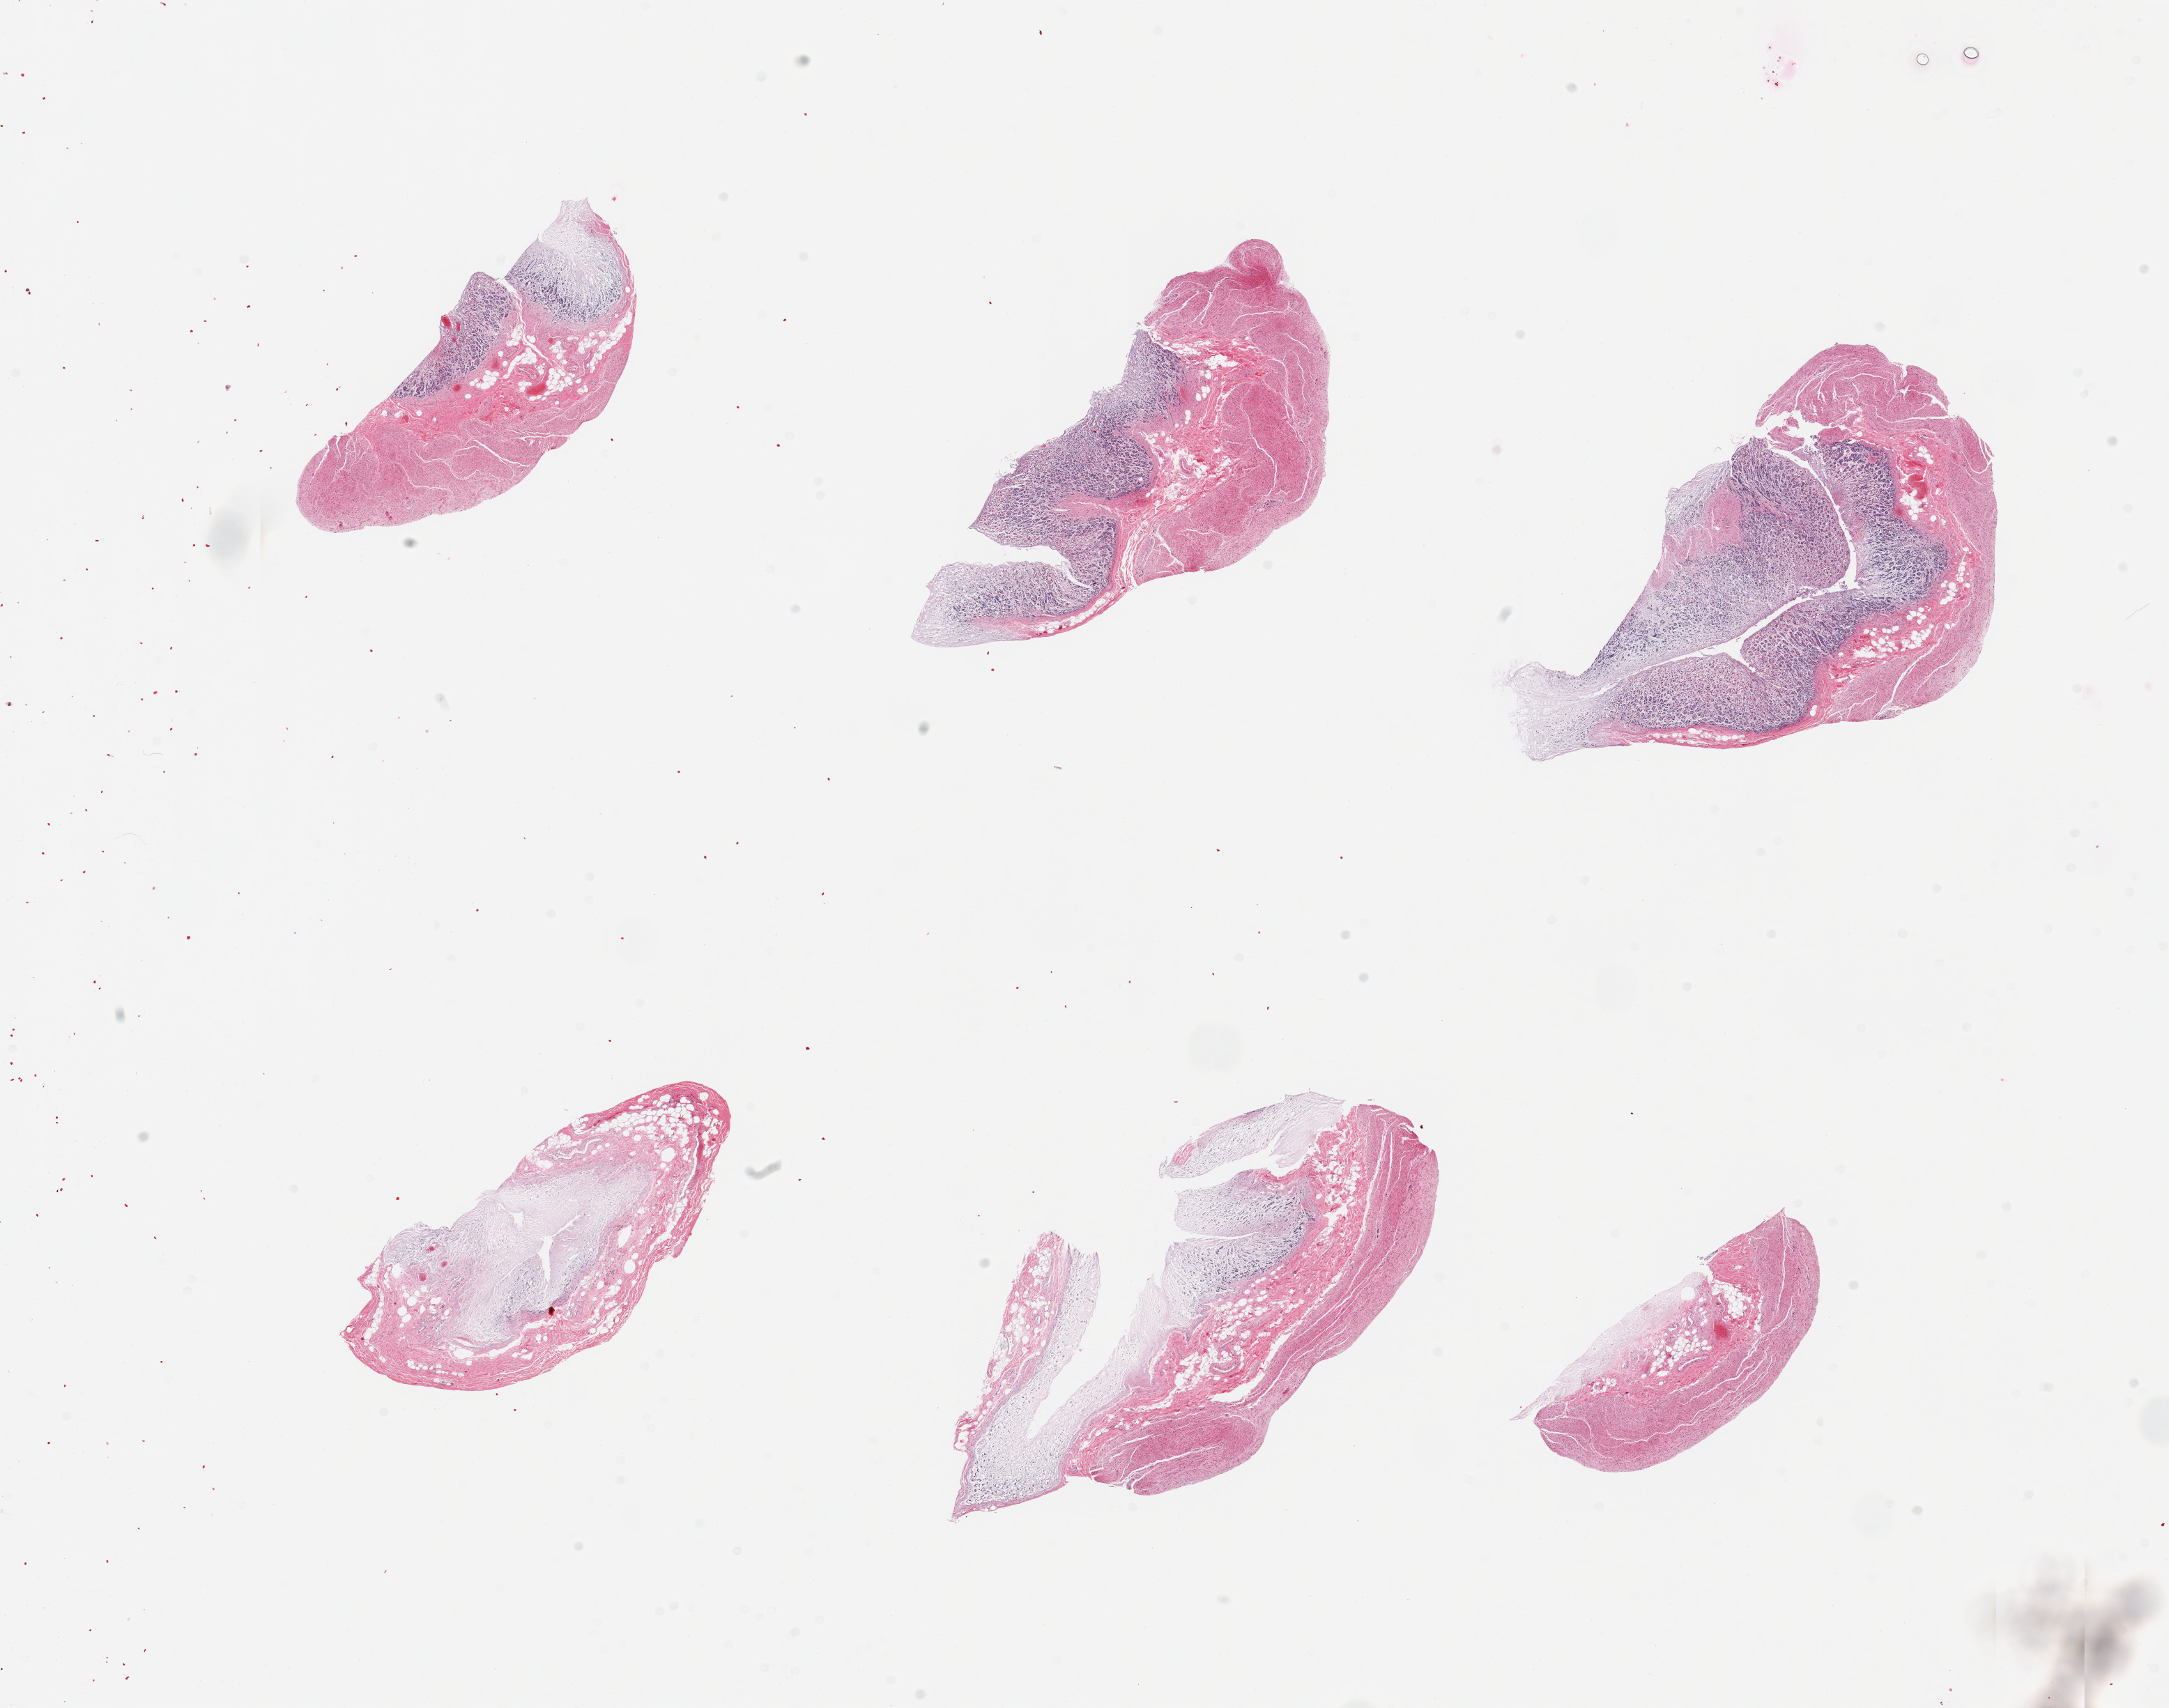
Digitized H&E-stained section, low-resolution overview of the scanned area, about 24.6 x 19.4 mm, PAXgene-fixed paraffin-embedded (PFPE) section, sampled site (target tissue): stomach, tissue donor sample. Donor sex: male.
Reviewer comment on this tissue sample: 6 pieces; predominantly full thickness sections, severe autolysis.